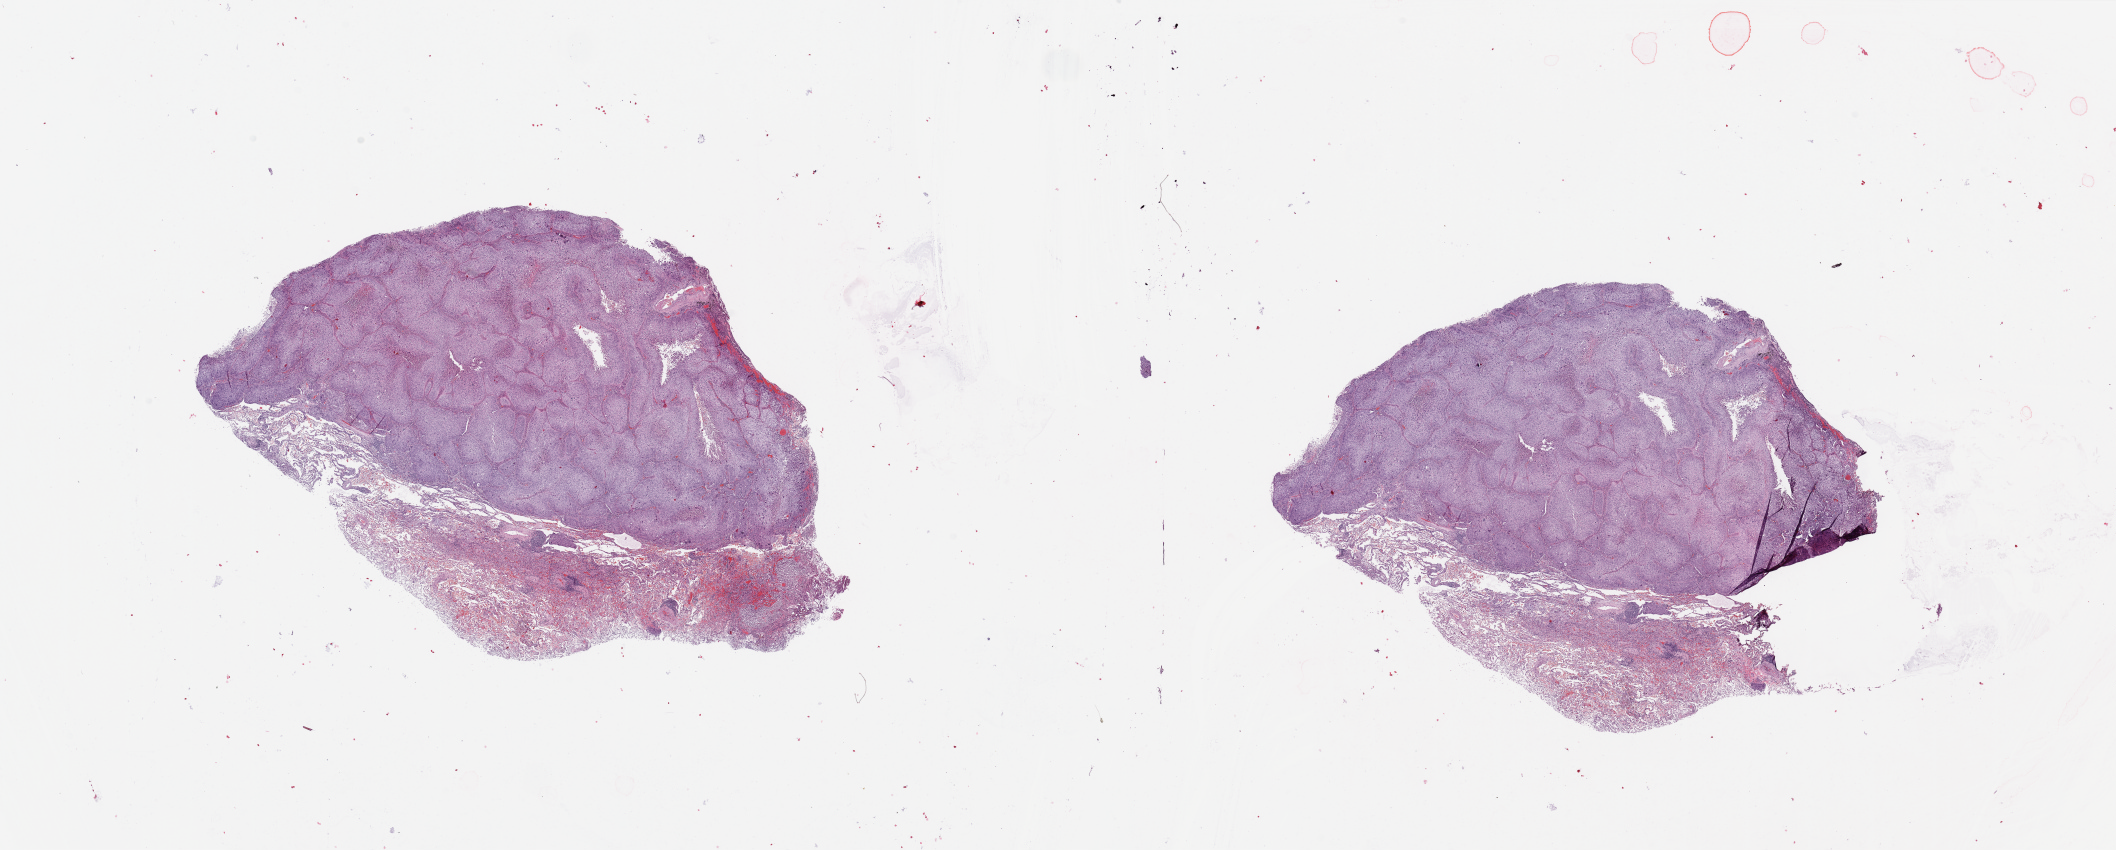
Hematoxylin and eosin (H&E) stained whole-slide image, a low-resolution overview of the entire scanned area, about 33.5 x 13.4 mm (from a 20x scan), tumour tissue sample, sampled site: lung. 64-year-old female patient. Slide review estimates, as recorded: tumour nuclei 70%, necrosis 10%.
Diagnosis: Squamous cell carcinoma, NOS.